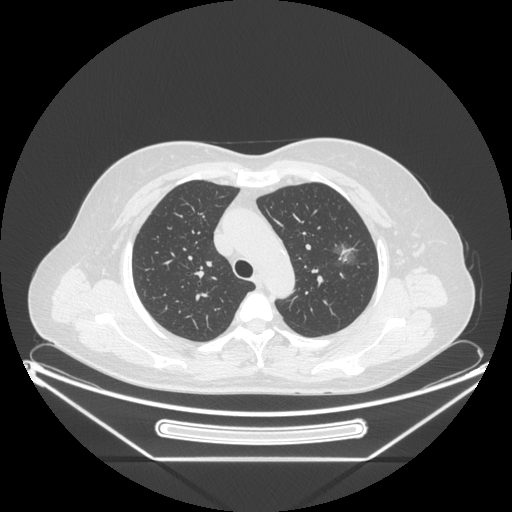
Chest CT, one axial slice. Position 160 of 226 along the scan axis. Reconstruction kernel STANDARD. 120 kVp. Lung window (W 1500 / L -600 HU). 512 × 512 image matrix, field of view 447 × 447 mm. Female patient, age 54 years. From the clinical record (not read from this slice): clinical TNM (as recorded): T1c N0 M0.
Outlined on this slice (rectangle marked by the reading radiologist):
- lung tumour (recorded histology: adenocarcinoma): box from (x=330, y=236) to (x=362, y=282) px